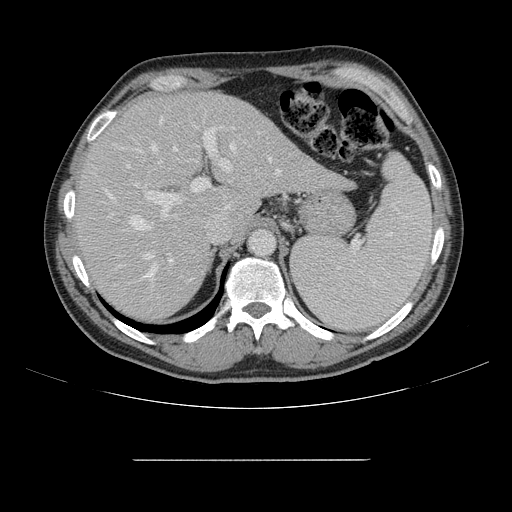
Contrast-enhanced abdominal CT, one axial slice. Slice 108 of 164 in the series (ordered by position). 120 kVp. Intravenous contrast given. Soft-tissue window (W 400 / L 40 HU). 2.5 mm slice thickness. 512 × 512 image matrix, field of view 404 × 404 mm. Male patient, age 54 years. Case-level facts recorded for this patient, not image findings: diagnosis: colorectal cancer liver metastases, imaged before liver resection; multiple liver metastases: yes; largest metastasis: 1 cm; disease in both lobes: no.
Outlined on this slice (outlined manually by an expert reader):
- hepatic veins: bounding box (x1, y1, x2, y2) in pixels: (105, 119, 281, 277)
- liver: (76, 94, 347, 320)
- planned liver remnant (the part of the liver to remain after resection): (77, 94, 241, 320)
- portal vein (with intrahepatic branches): (124, 127, 231, 299)